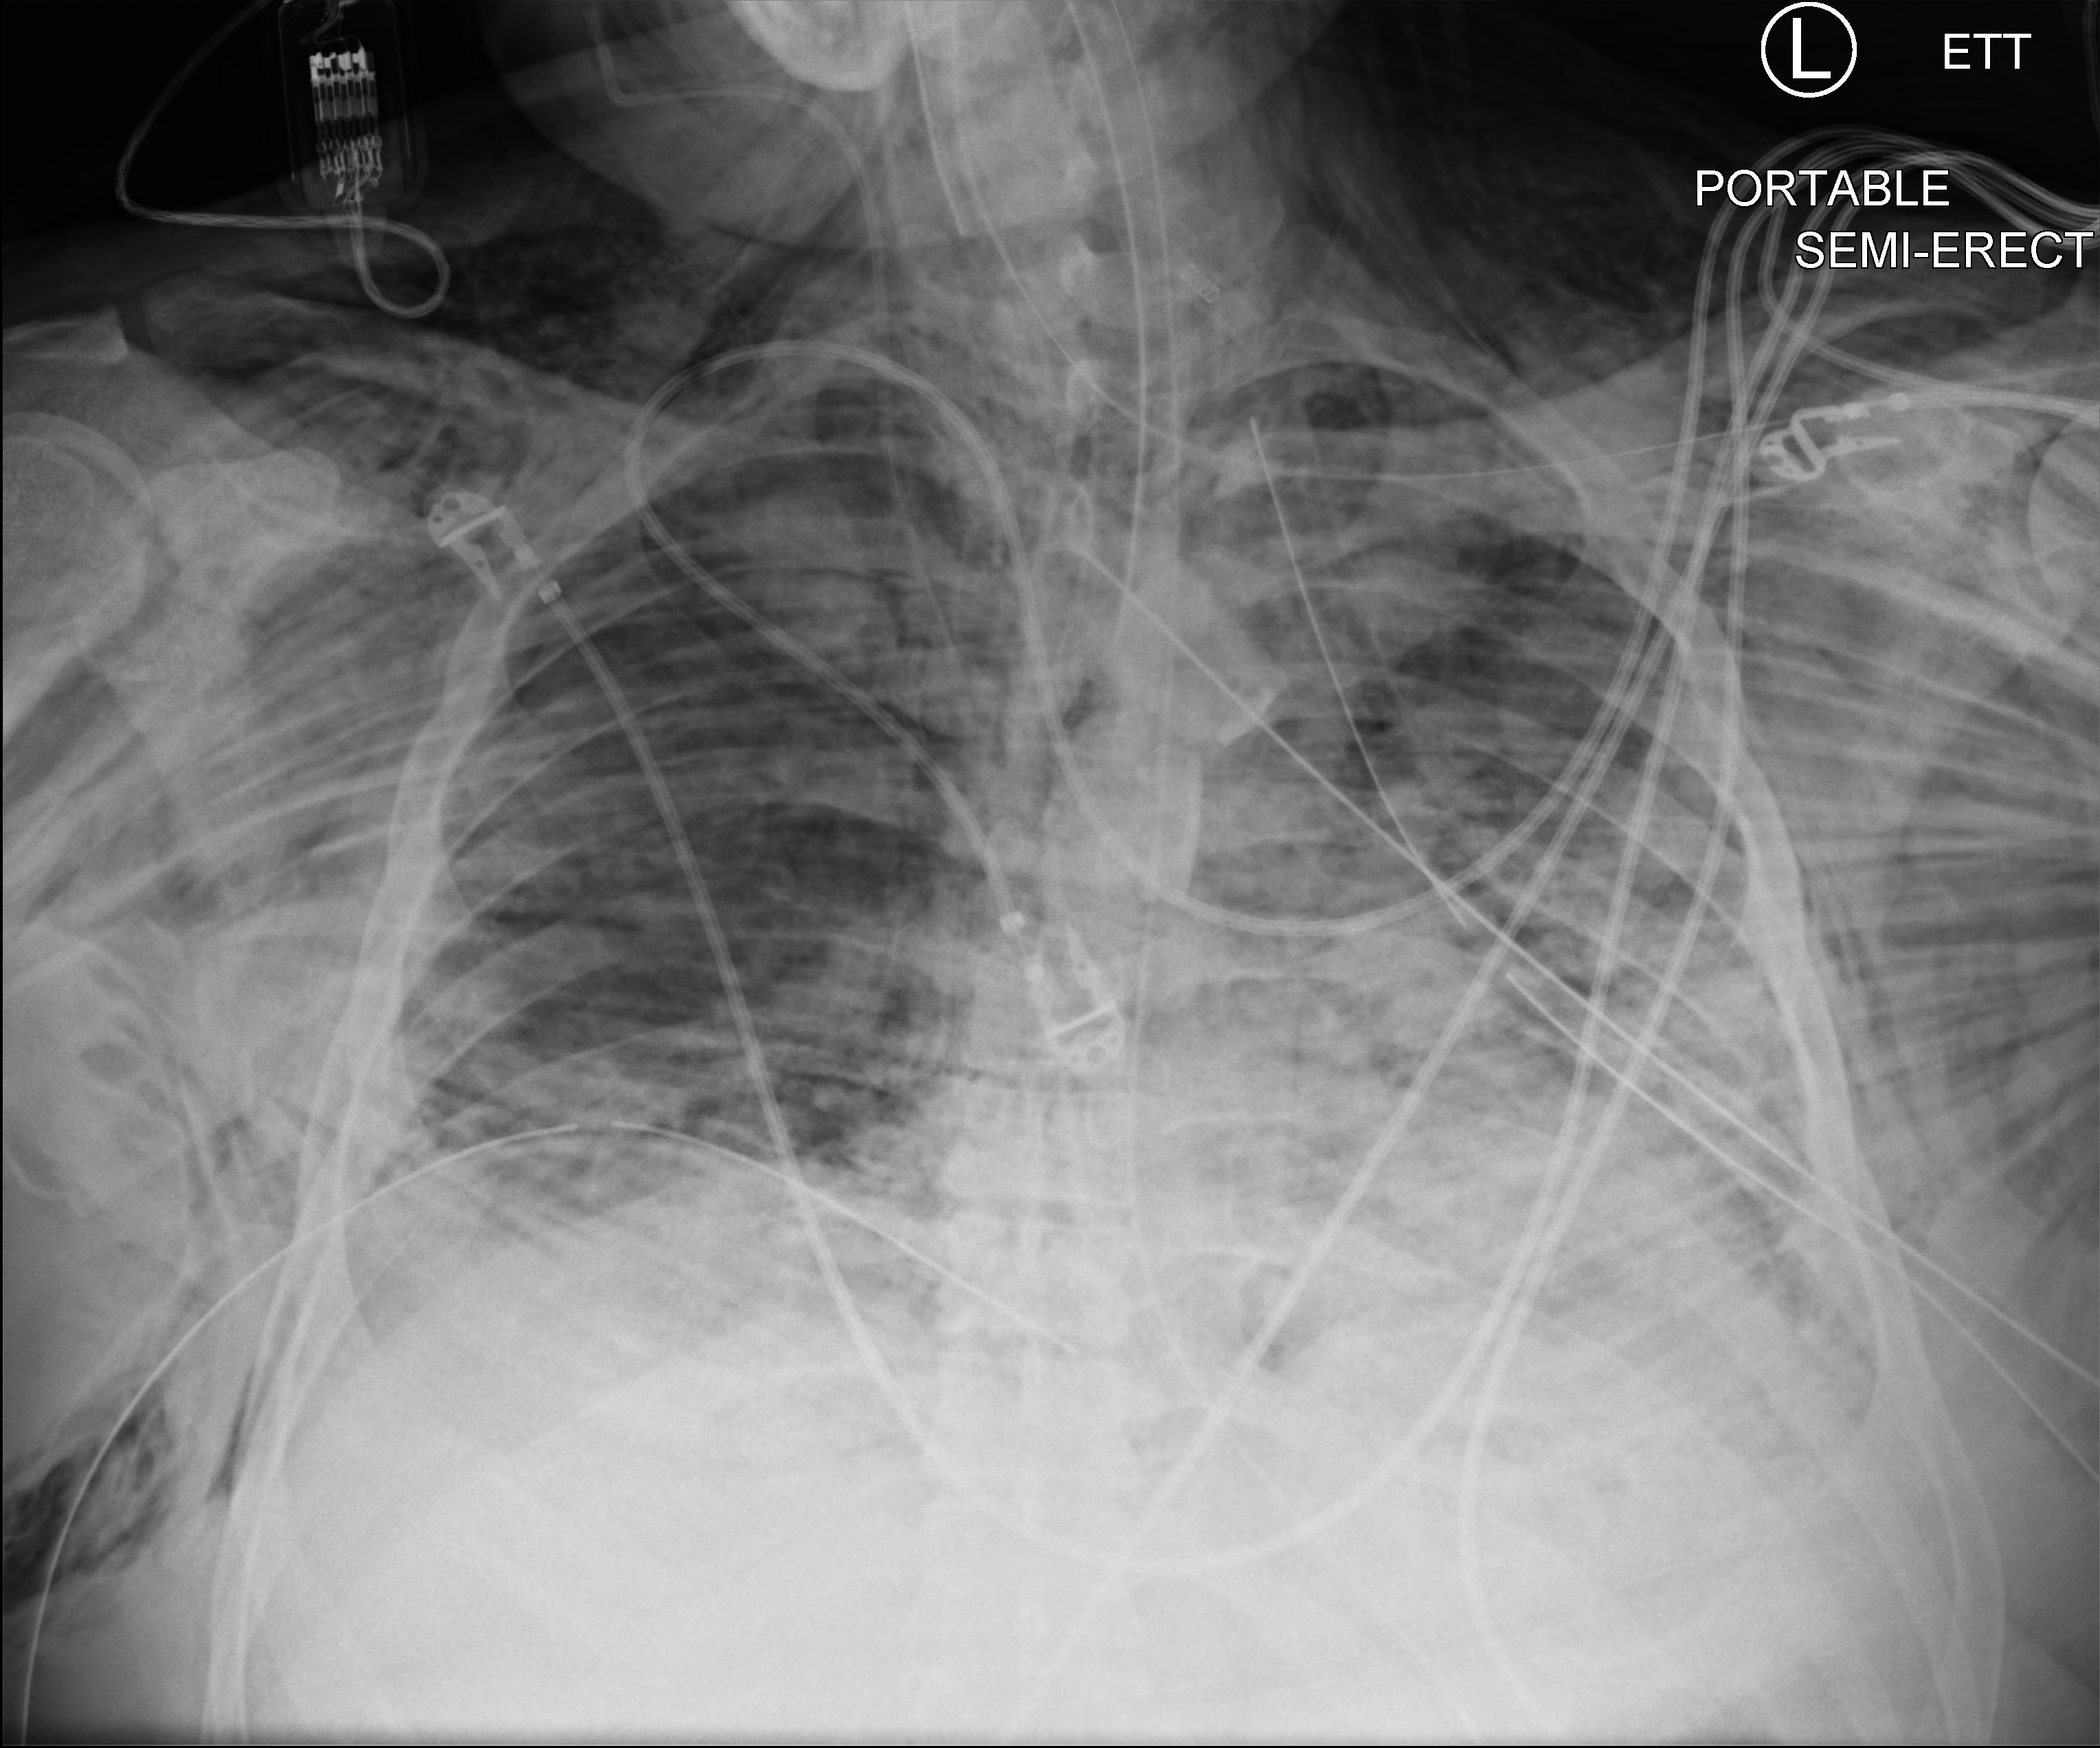
Chest X-ray (portable). Male patient hospitalised with COVID-19, age 18–59 years.
Admission-level facts for this patient (not findings on this image; timing relative to this image not recorded):
- mechanically ventilated during this hospital stay: yes
- length of hospital stay: 29 days
- admitted to intensive care during this hospital stay: yes